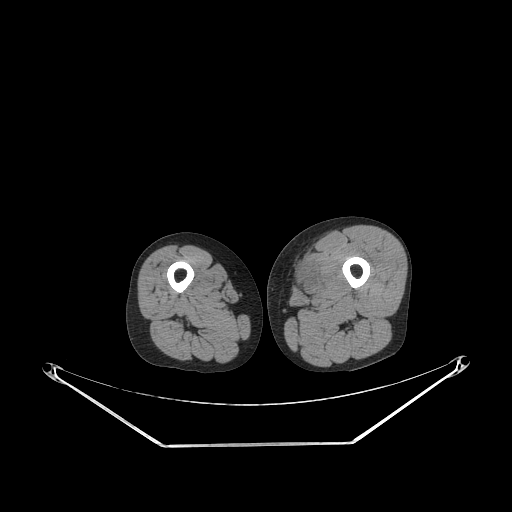
CT of an extremity soft-tissue mass (from a PET/CT study), one axial slice. Slice 228 of 267 in the series (ordered by position). 140 kVp. Soft-tissue window (W 400 / L 40 HU). 3.75 mm slice thickness. 512 × 512 image matrix, field of view 500 × 500 mm. Male patient. From the clinical record (not read from this slice): histological type: pleiomorphic leiomyosarcoma; grade: high; site of the primary tumour: left thigh.
Structures marked on this image (expert contour drawn on MRI and transferred to this co-registered scan by the dataset authors):
- gross tumour volume including surrounding oedema: box from (x=290, y=256) to (x=321, y=293) px
- gross tumour volume (mass): (x=294, y=262)–(x=314, y=291)